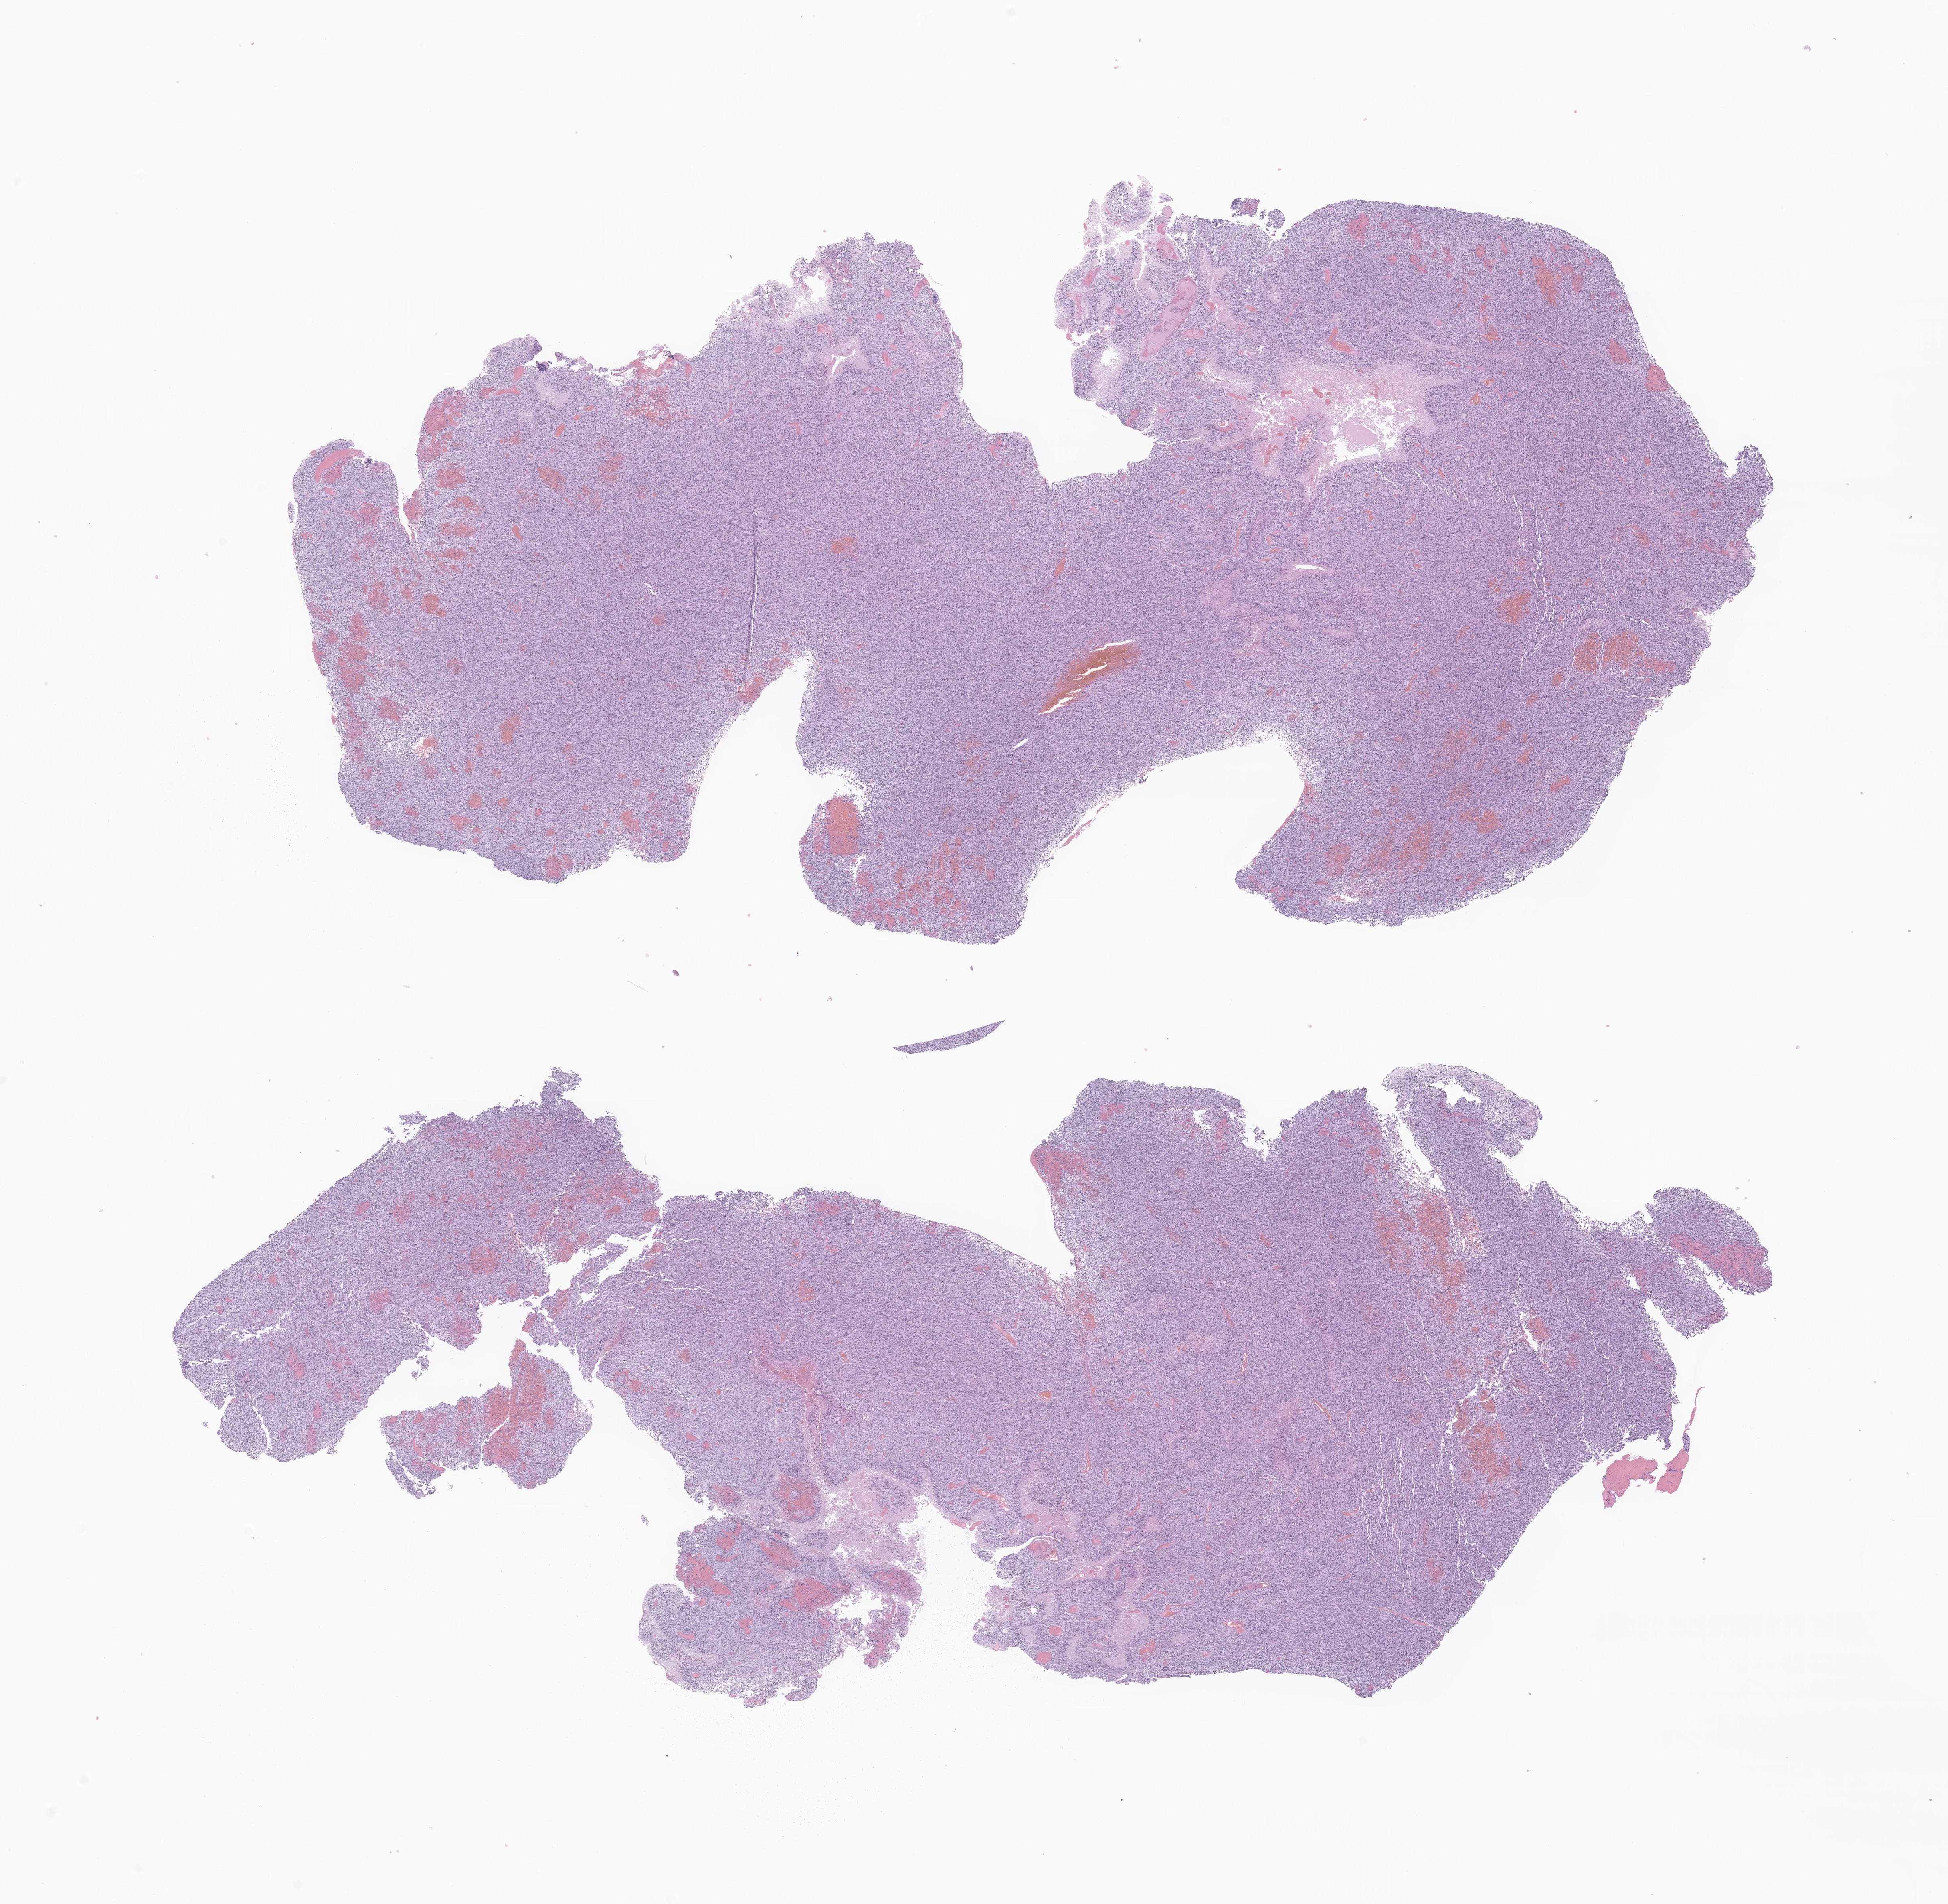
Whole-slide image, H&E stain of tumor tissue from the parietal lobe, low-resolution overview of the scanned area, about 20.6 x 20.1 mm, FFPE section. Patient: female, age 215 months (17 years 11 months).
Recorded diagnosis: Glioma, malignant.